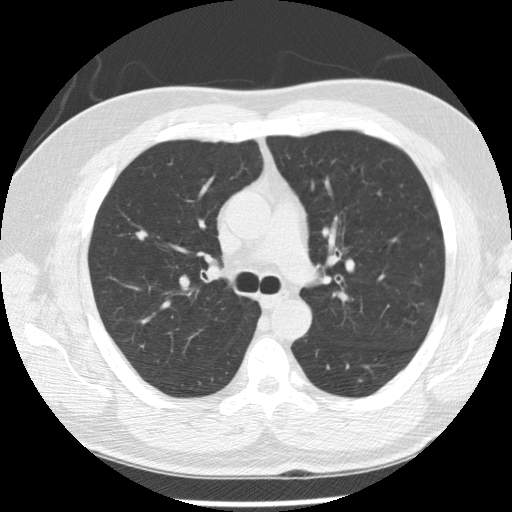
Low-dose screening chest CT, axial slice; baseline annual screen; lung window (W 1500 / L -600 HU); 120 kVp; slice 91 of 265 in the series; 512 × 512 image matrix. Male, age 57 years at enrolment.
Expert reader's lesion annotation, bounding box (x1, y1, x2, y2) in pixels: (123, 219, 157, 252). Screening reader's record for this exam (one nodule recorded; not confirmed to be the boxed lesion): non-calcified nodule or mass ≥4 mm, right upper lobe, 7 × 7 mm, poorly defined margins, soft tissue attenuation. Official screen result: positive, change unspecified: nodule(s) >= 4 mm or enlarging nodule(s), mass(es), or other non-specific abnormalities suspicious for lung cancer. Participant outcome: lung cancer diagnosed 125 days after this screen — squamous cell carcinoma, NOS, right upper lobe, moderately differentiated (G2), stage IA (AJCC 6th edition), 10 mm at pathology.